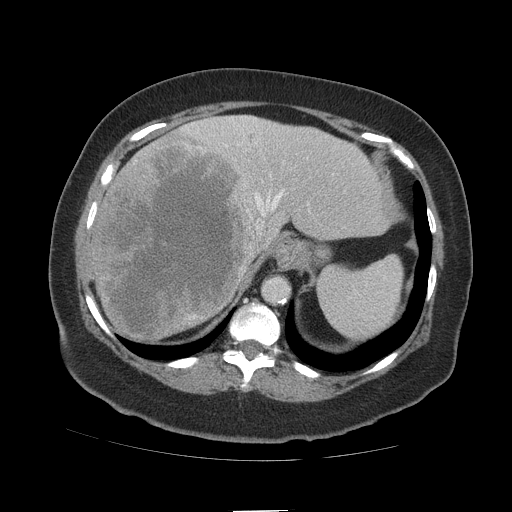
Contrast-enhanced abdominal CT (liver protocol), one axial slice; slice 83 of 109 in the series (ordered by position); reconstruction kernel STANDARD; soft-tissue window (W 400 / L 40 HU); 2.5 mm slice thickness; 512 × 512 image matrix, field of view 420 × 420 mm. Case-level facts recorded for this patient, not image findings: diagnosis: hepatocellular carcinoma (patient treated with transarterial chemoembolisation; whether this scan precedes or follows treatment is not stated here); TNM stage (as recorded): Stage-IVB; Child-Pugh class: A; tumour differentiation: poorly differentiated; tumour nodularity: multinodular.
Outlined on this slice (semi-automatically segmented with operator editing):
- liver parenchyma outside the tumour (the mass and vessels are separate outlines, so this box may not span the whole liver): box from (x=88, y=114) to (x=392, y=340) px
- mass: (x=93, y=133)–(x=265, y=339)
- liver vessels: (x=185, y=117)–(x=284, y=221)